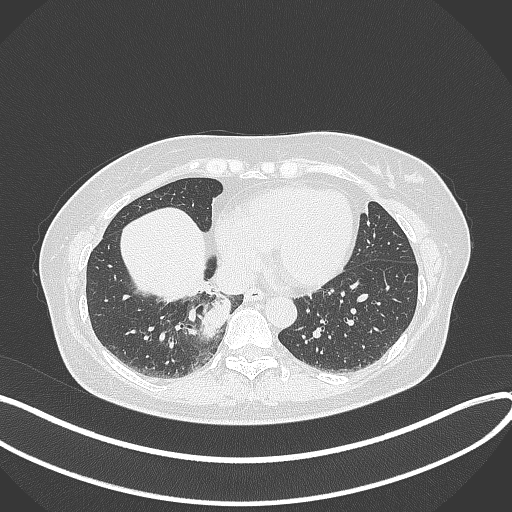
Chest CT, one axial slice. Slice 109 of 331 in the series (ordered by position). Reconstruction kernel B70f. 120 kVp. Lung window (W 1500 / L -600 HU). 1 mm slice thickness. 512 × 512 image matrix, field of view 400 × 400 mm. Patient: female, 54 years. Case-level facts recorded for this patient, not image findings: clinical TNM (as recorded): T4 N0 M0.
Outlined on this slice (bounding box drawn by a radiologist):
- lung tumour (recorded histology: adenocarcinoma): bounding box <196,289,235,345> (left, top, right, bottom; pixels)